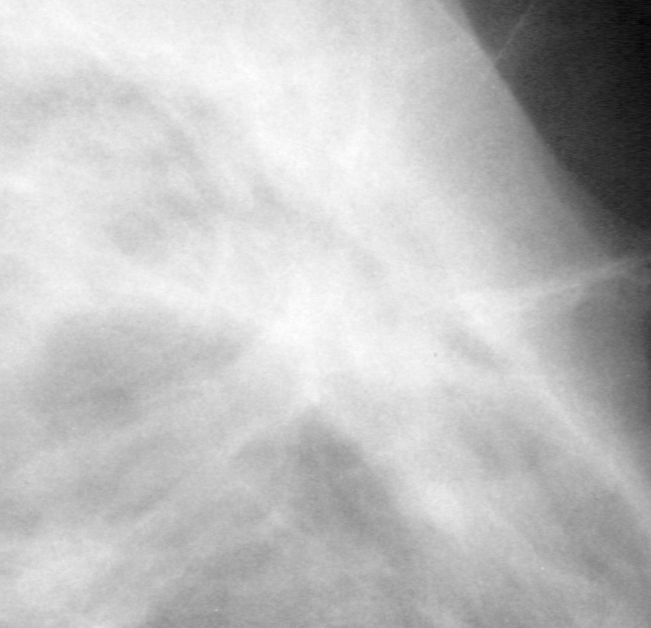
Crop from a digitized film mammogram around one marked abnormality, right breast, MLO view, BI-RADS breast density category 4 (scale 1–4).
- Finding: mass, shape irregular, margins spiculated; BI-RADS assessment category 5; subtlety rating 2 on a 1 (subtle) to 5 (obvious) scale; pathology result (as recorded, not read from the image): malignant.